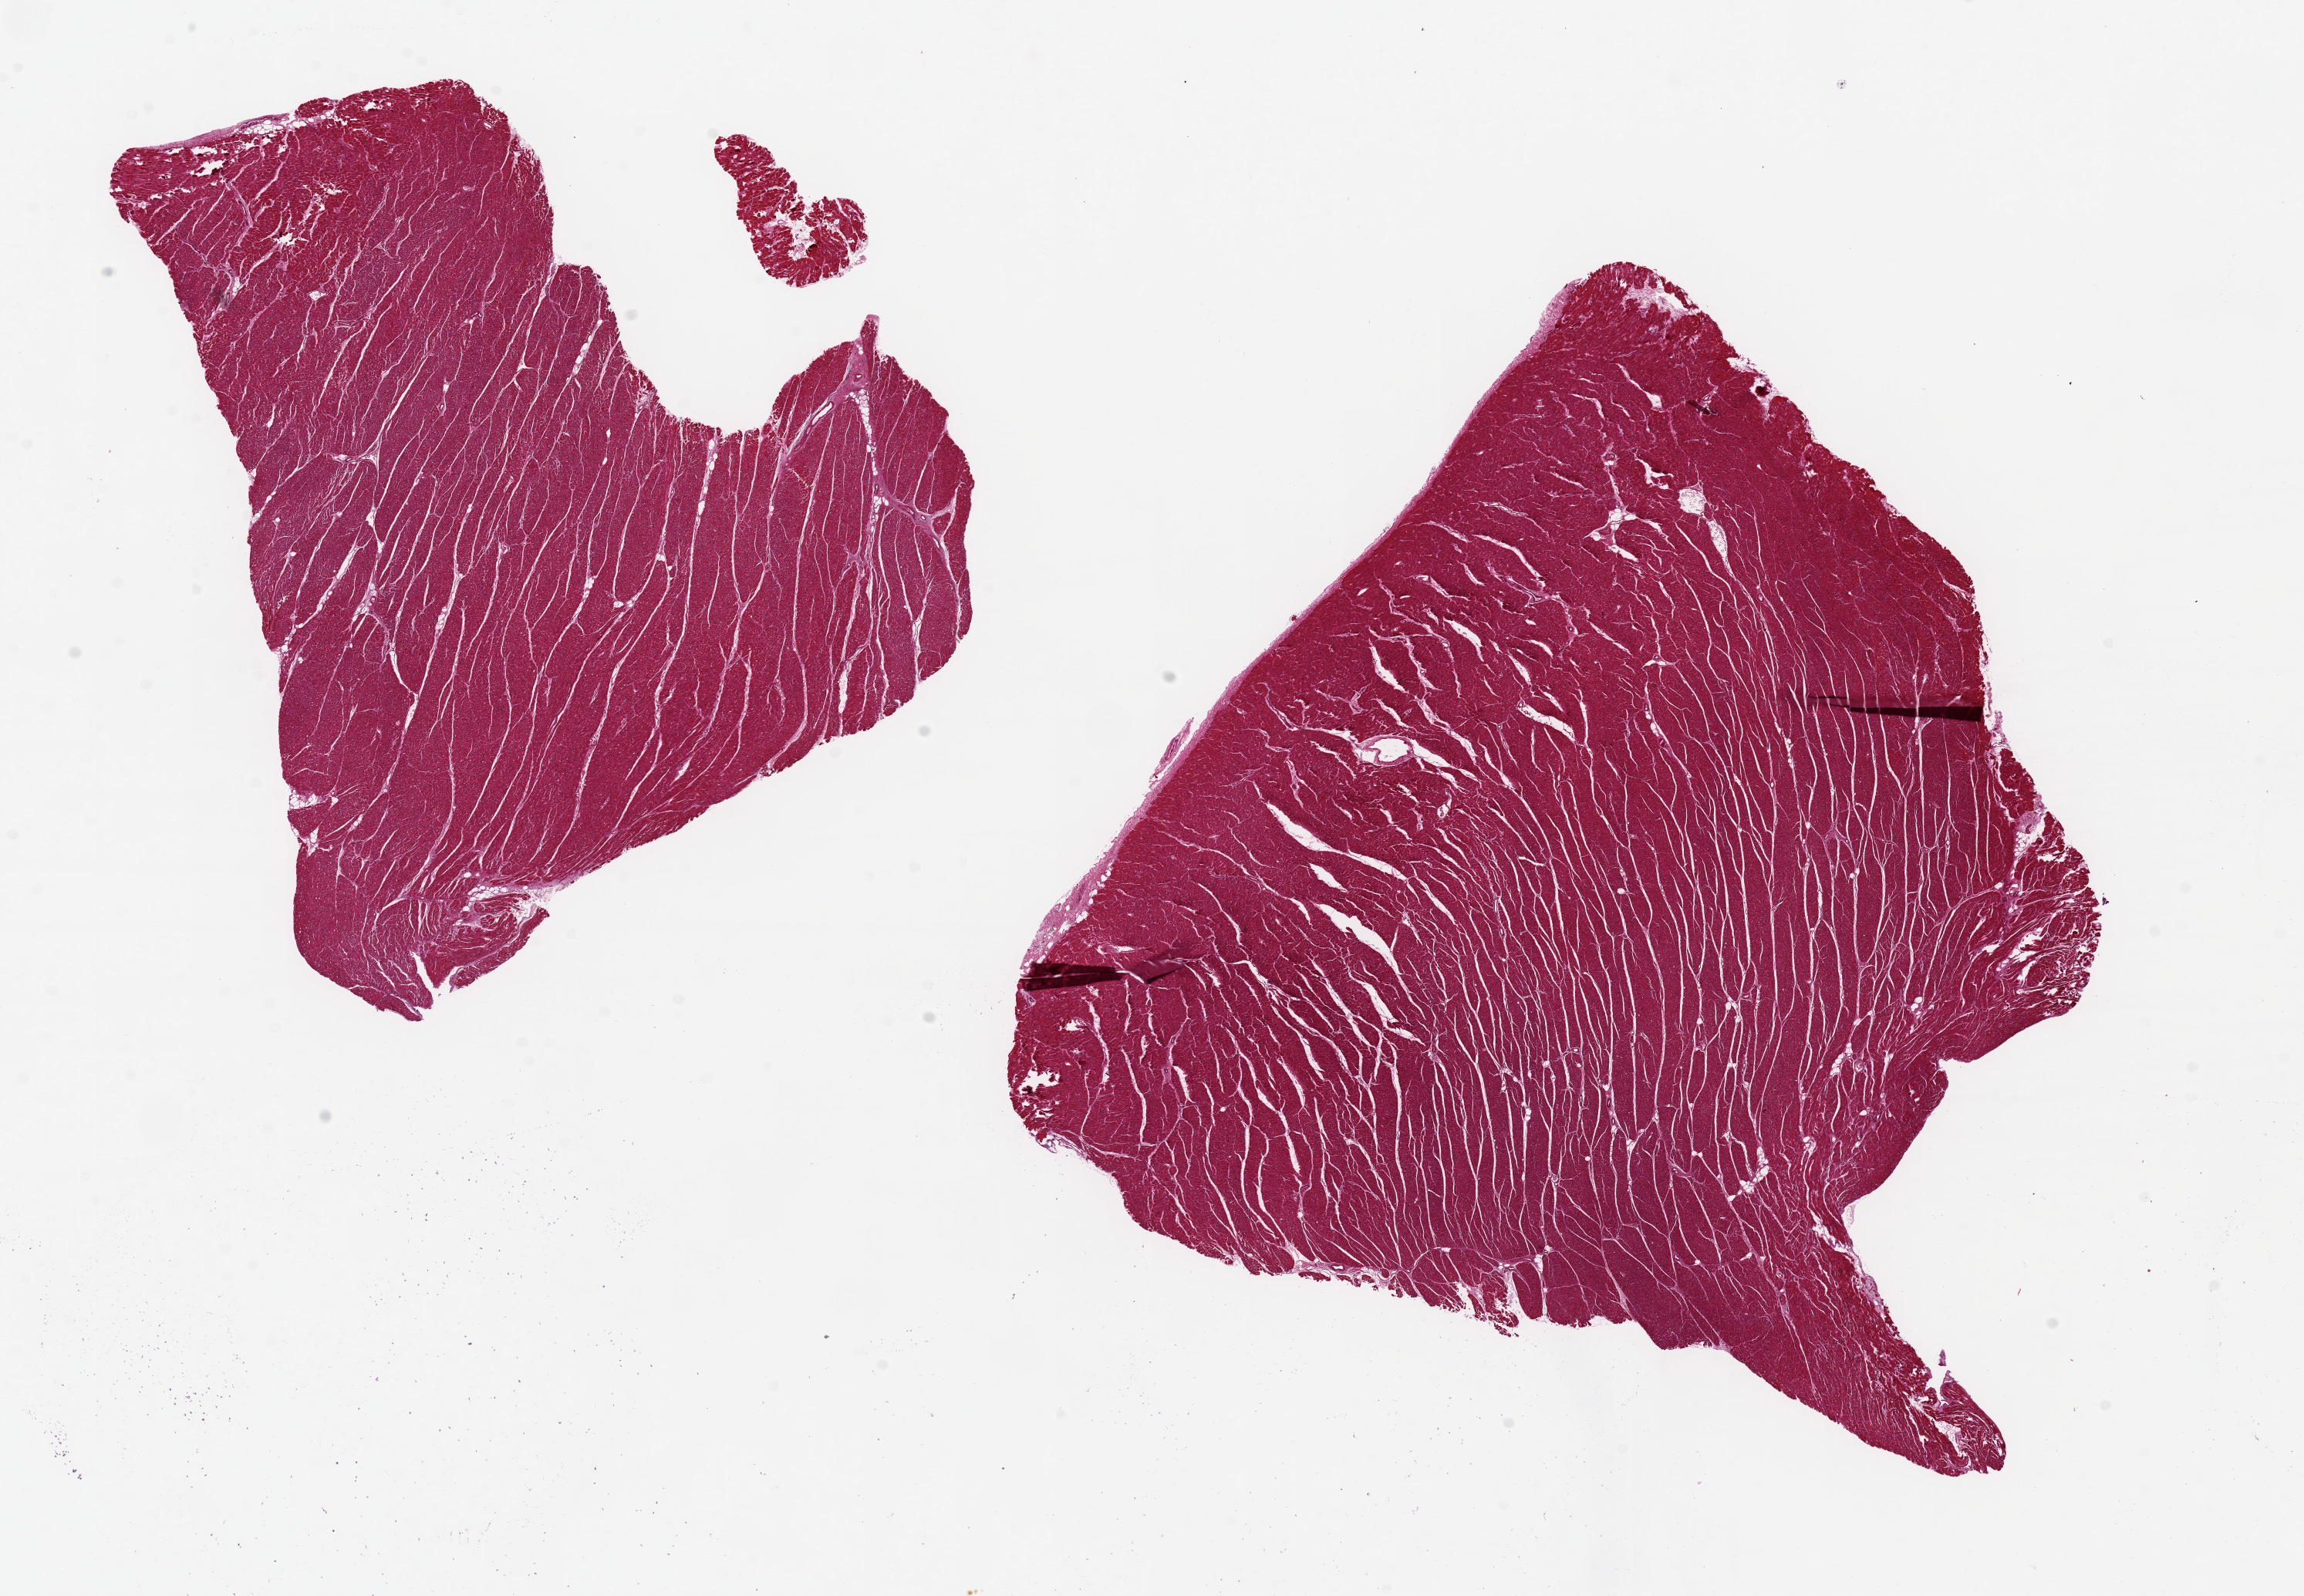
H&E whole-slide image — low-resolution overview of the scanned area, about 23.6 x 16.4 mm; PAXgene-fixed, paraffin-embedded tissue; target tissue: heart; donor tissue sample.
Review note (as recorded): 2 pieces ~10x9mm. Minimal ischemic changes.